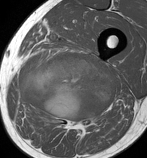
MRI of an extremity soft-tissue mass, one axial slice. Slice 61 of 86 in the series (ordered by position). MR volume resampled by the dataset authors to the PET/CT grid (not the native acquisition matrix). 147 × 158 image matrix. Male patient. From the clinical record (not read from this slice): histological type: undifferentiated pleomorphic liposarcoma; grade: high; site of the primary tumour: left thigh.
Structures marked on this image (expert contour drawn on MRI and transferred to this co-registered scan by the dataset authors):
- gross tumour volume including surrounding oedema: bounding box [x1, y1, x2, y2] px = [16, 53, 115, 130]
- gross tumour volume (mass): [21, 53, 115, 121]